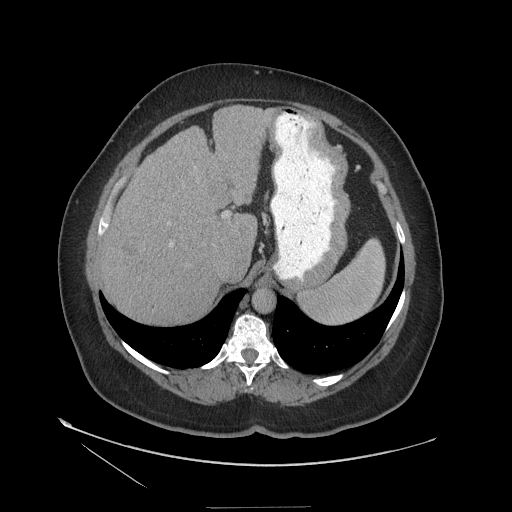
Contrast-enhanced abdominal CT (liver protocol), one axial slice. Position 86 of 127 along the scan axis. Soft-tissue window (W 400 / L 40 HU). 512 × 512 image matrix, field of view 480 × 480 mm. From the clinical record (not read from this slice): diagnosis: hepatocellular carcinoma (patient treated with transarterial chemoembolisation; whether this scan precedes or follows treatment is not stated here); TNM stage (as recorded): Stage-II; Child-Pugh class: A; tumour differentiation: well differentiated; tumour nodularity: multinodular.
Annotated regions visible in this slice (semi-automatically segmented with operator editing):
- abdominal aorta: box from (x=253, y=289) to (x=274, y=312) px
- liver parenchyma outside the tumour (the mass and vessels are separate outlines, so this box may not span the whole liver): (x=98, y=106)–(x=274, y=324)
- mass: (x=121, y=233)–(x=147, y=257)
- liver vessels: (x=170, y=212)–(x=228, y=246)